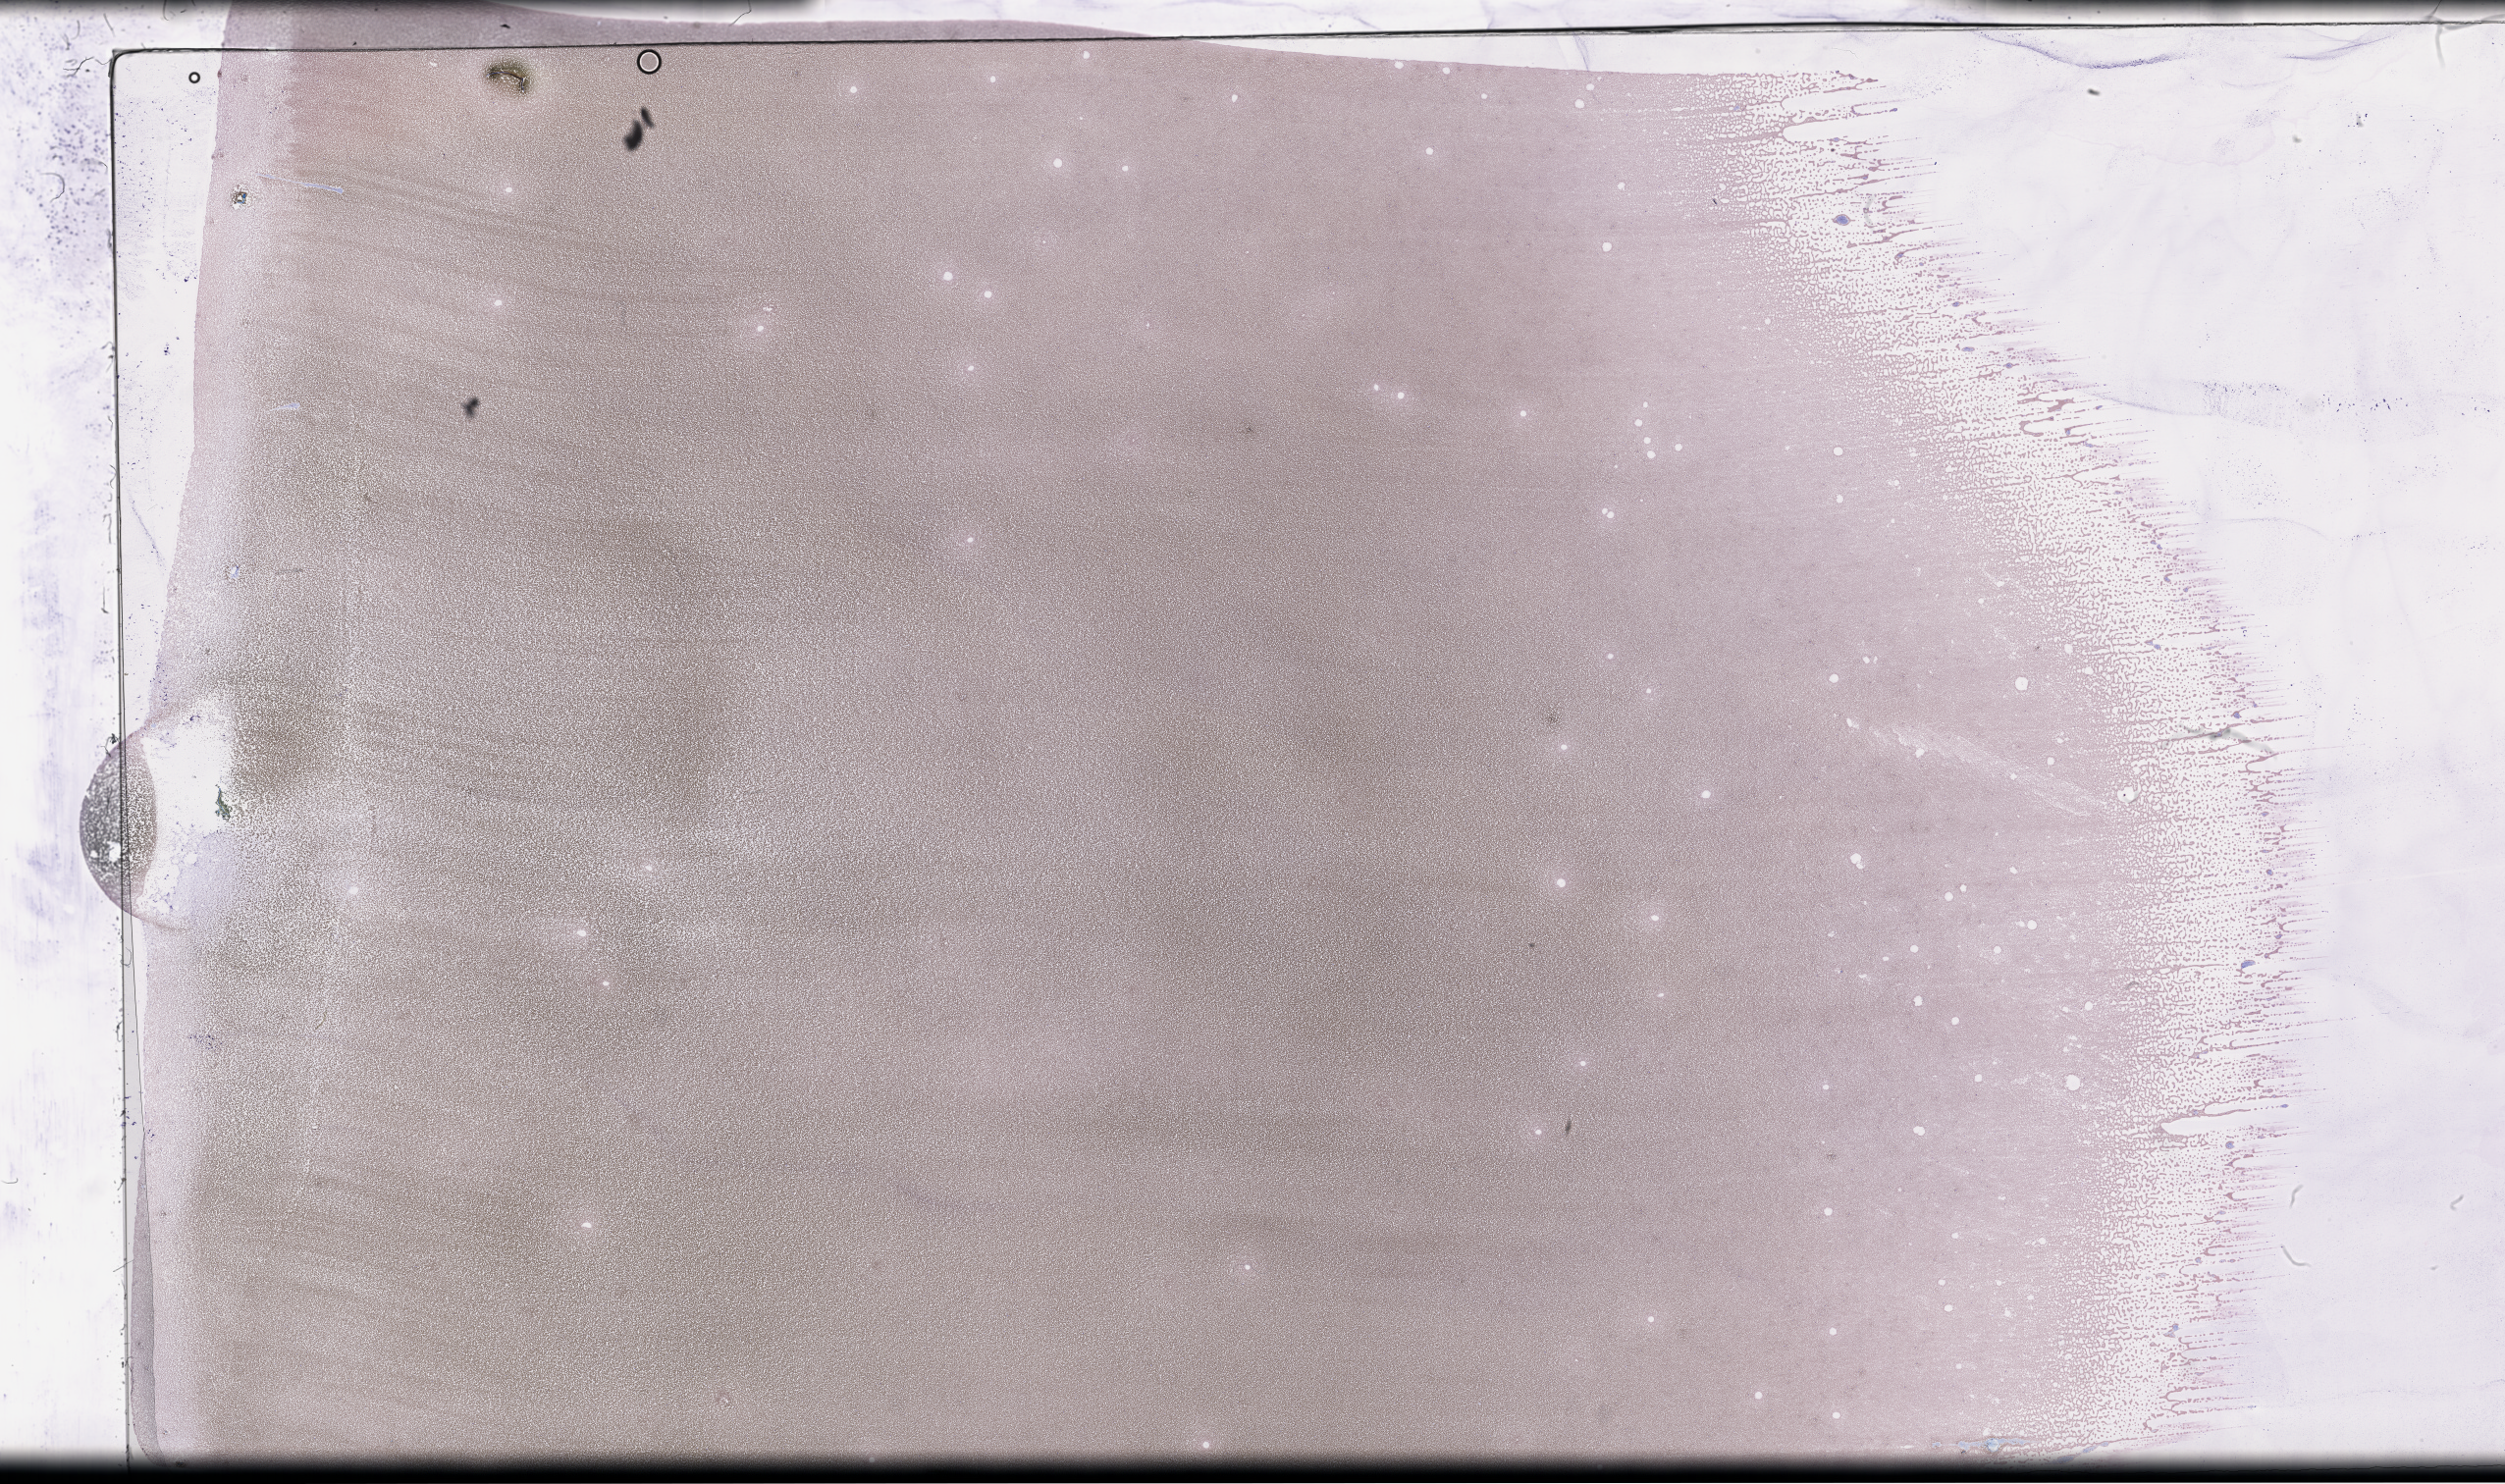
Whole-slide image of a whole blood smear, Wright–Giemsa stain — shown as a low-resolution overview of the whole scanned area (about 41.2 x 24.4 mm). Male patient.
* patient diagnosis: Plasma Cell Myeloma